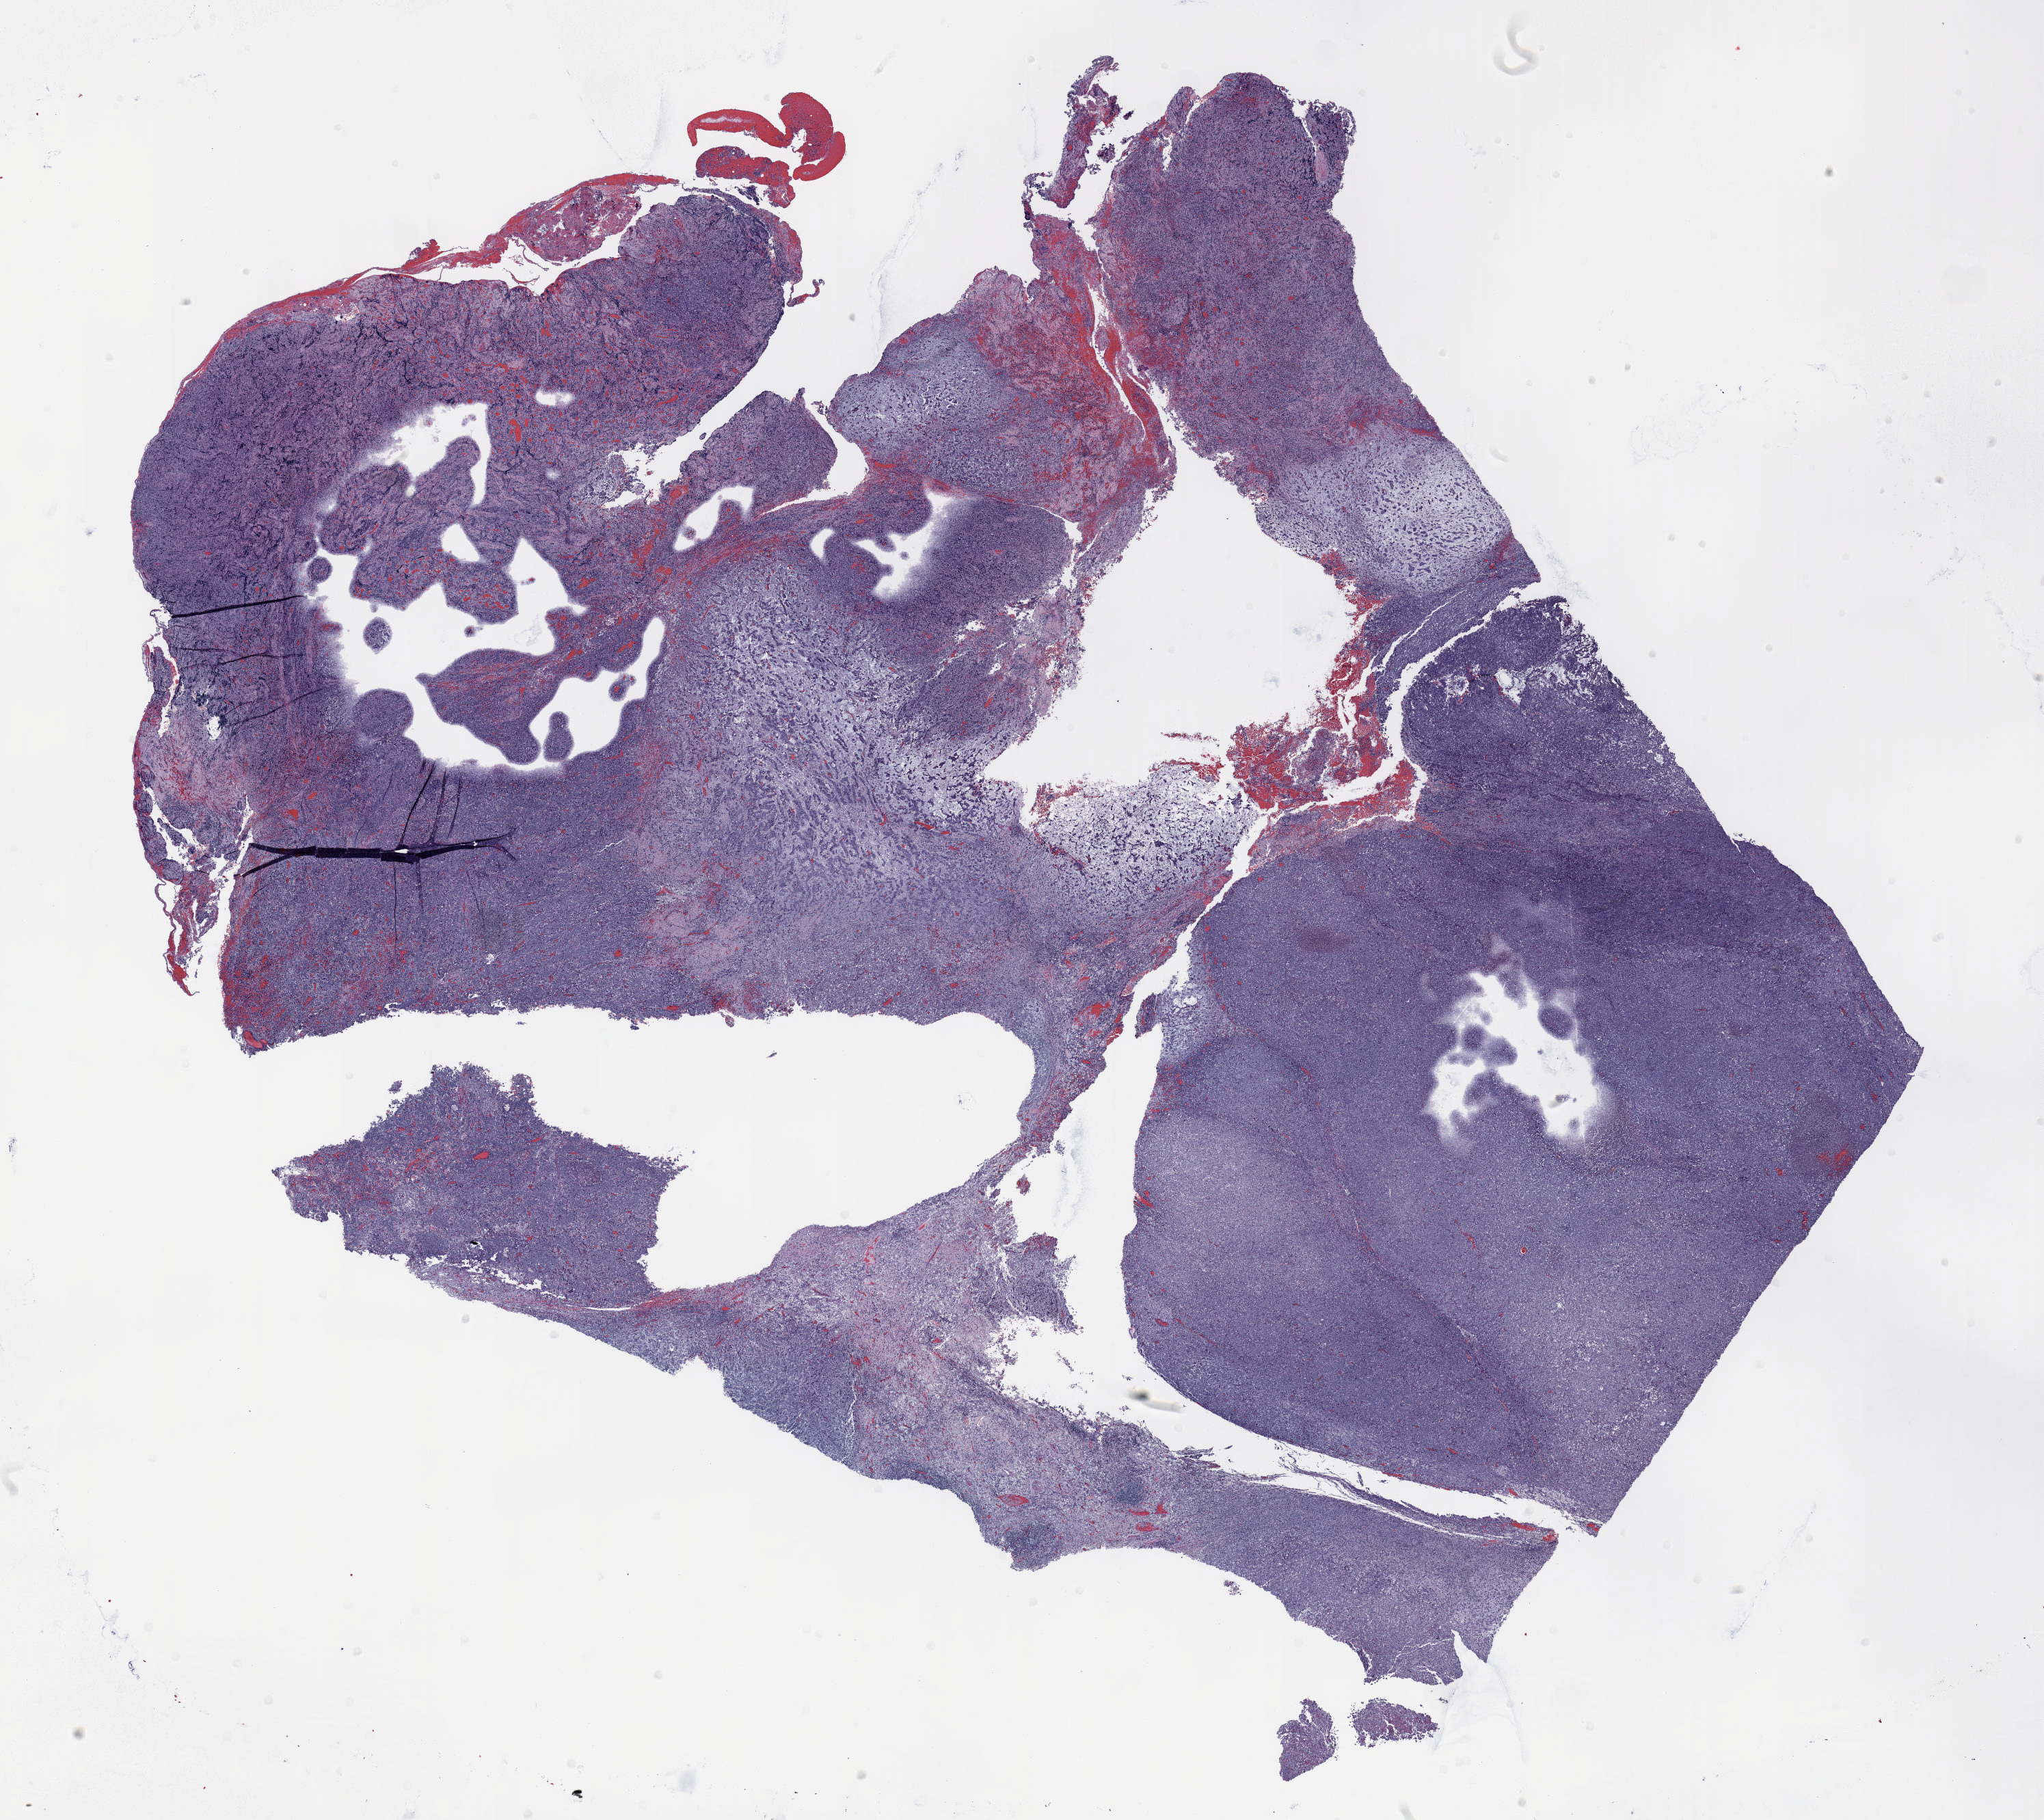
Whole-slide histology image, H&E-stained — low-resolution overview of the scanned area, about 24.0 x 21.4 mm (from a 20x scan); formalin-fixed paraffin-embedded (FFPE) section; lung. Male patient, aged 55 at enrolment. Current smoker at enrolment. Grade: poorly differentiated (G3).
* participant's lung-cancer diagnosis: Adenocarcinoma, NOS
* tumour size (pathology): 115 mm
* primary tumour location (clinical record): right upper lobe
* stage (AJCC 6th edition): IIB